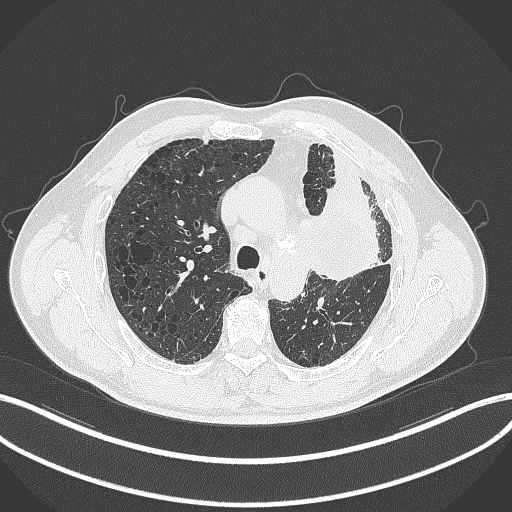
Chest CT, one axial slice. Reconstruction kernel B70f. Lung window (W 1500 / L -600 HU). 512 × 512 image matrix, field of view 400 × 400 mm. Male patient, age 68 years. Case-level facts recorded for this patient, not image findings: clinical TNM (as recorded): T3 N3 M1.
Outlined on this slice (rectangle marked by the reading radiologist):
- lung tumour (recorded histology: adenocarcinoma): box from (x=301, y=178) to (x=382, y=285) px